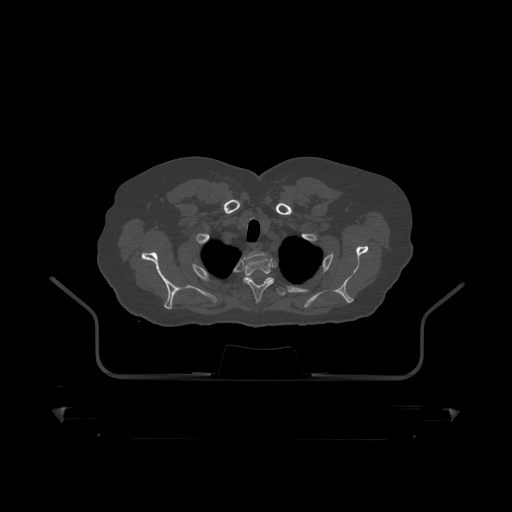
CT including the spine, one axial slice; position 373 of 390 along the scan axis; reconstruction kernel STANDARD; bone window (W 1800 / L 400 HU); 512 × 512 image matrix, field of view 650 × 650 mm. Male patient, age 60 years. From the clinical record (not read from this slice): primary cancer: prostate.
Structures marked on this image (semi-automatically segmented with operator editing):
- T1 vertebra: bounding box <240,252,262,268> (left, top, right, bottom; pixels)
- T2 vertebra: <243,257,275,302>
- T3 vertebra: <234,277,287,297>